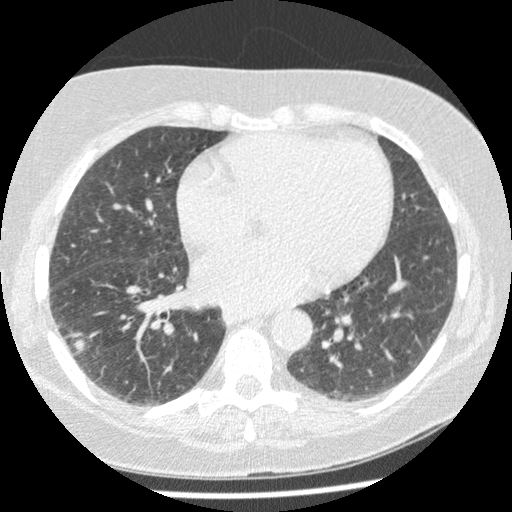
Low-dose screening chest CT, one axial slice; slice 103 of 241 in the series (ordered by position); reconstruction kernel STANDARD; 120 kVp; lung window (W 1500 / L -600 HU); 1.25 mm slice thickness; 512 × 512 image matrix, field of view 305 × 305 mm.
Outlined on this slice (manually delineated by an expert):
- lesion 1 (tumor, lower lobe of right lung): bounding box (x1, y1, x2, y2) in pixels: (72, 339, 89, 355)